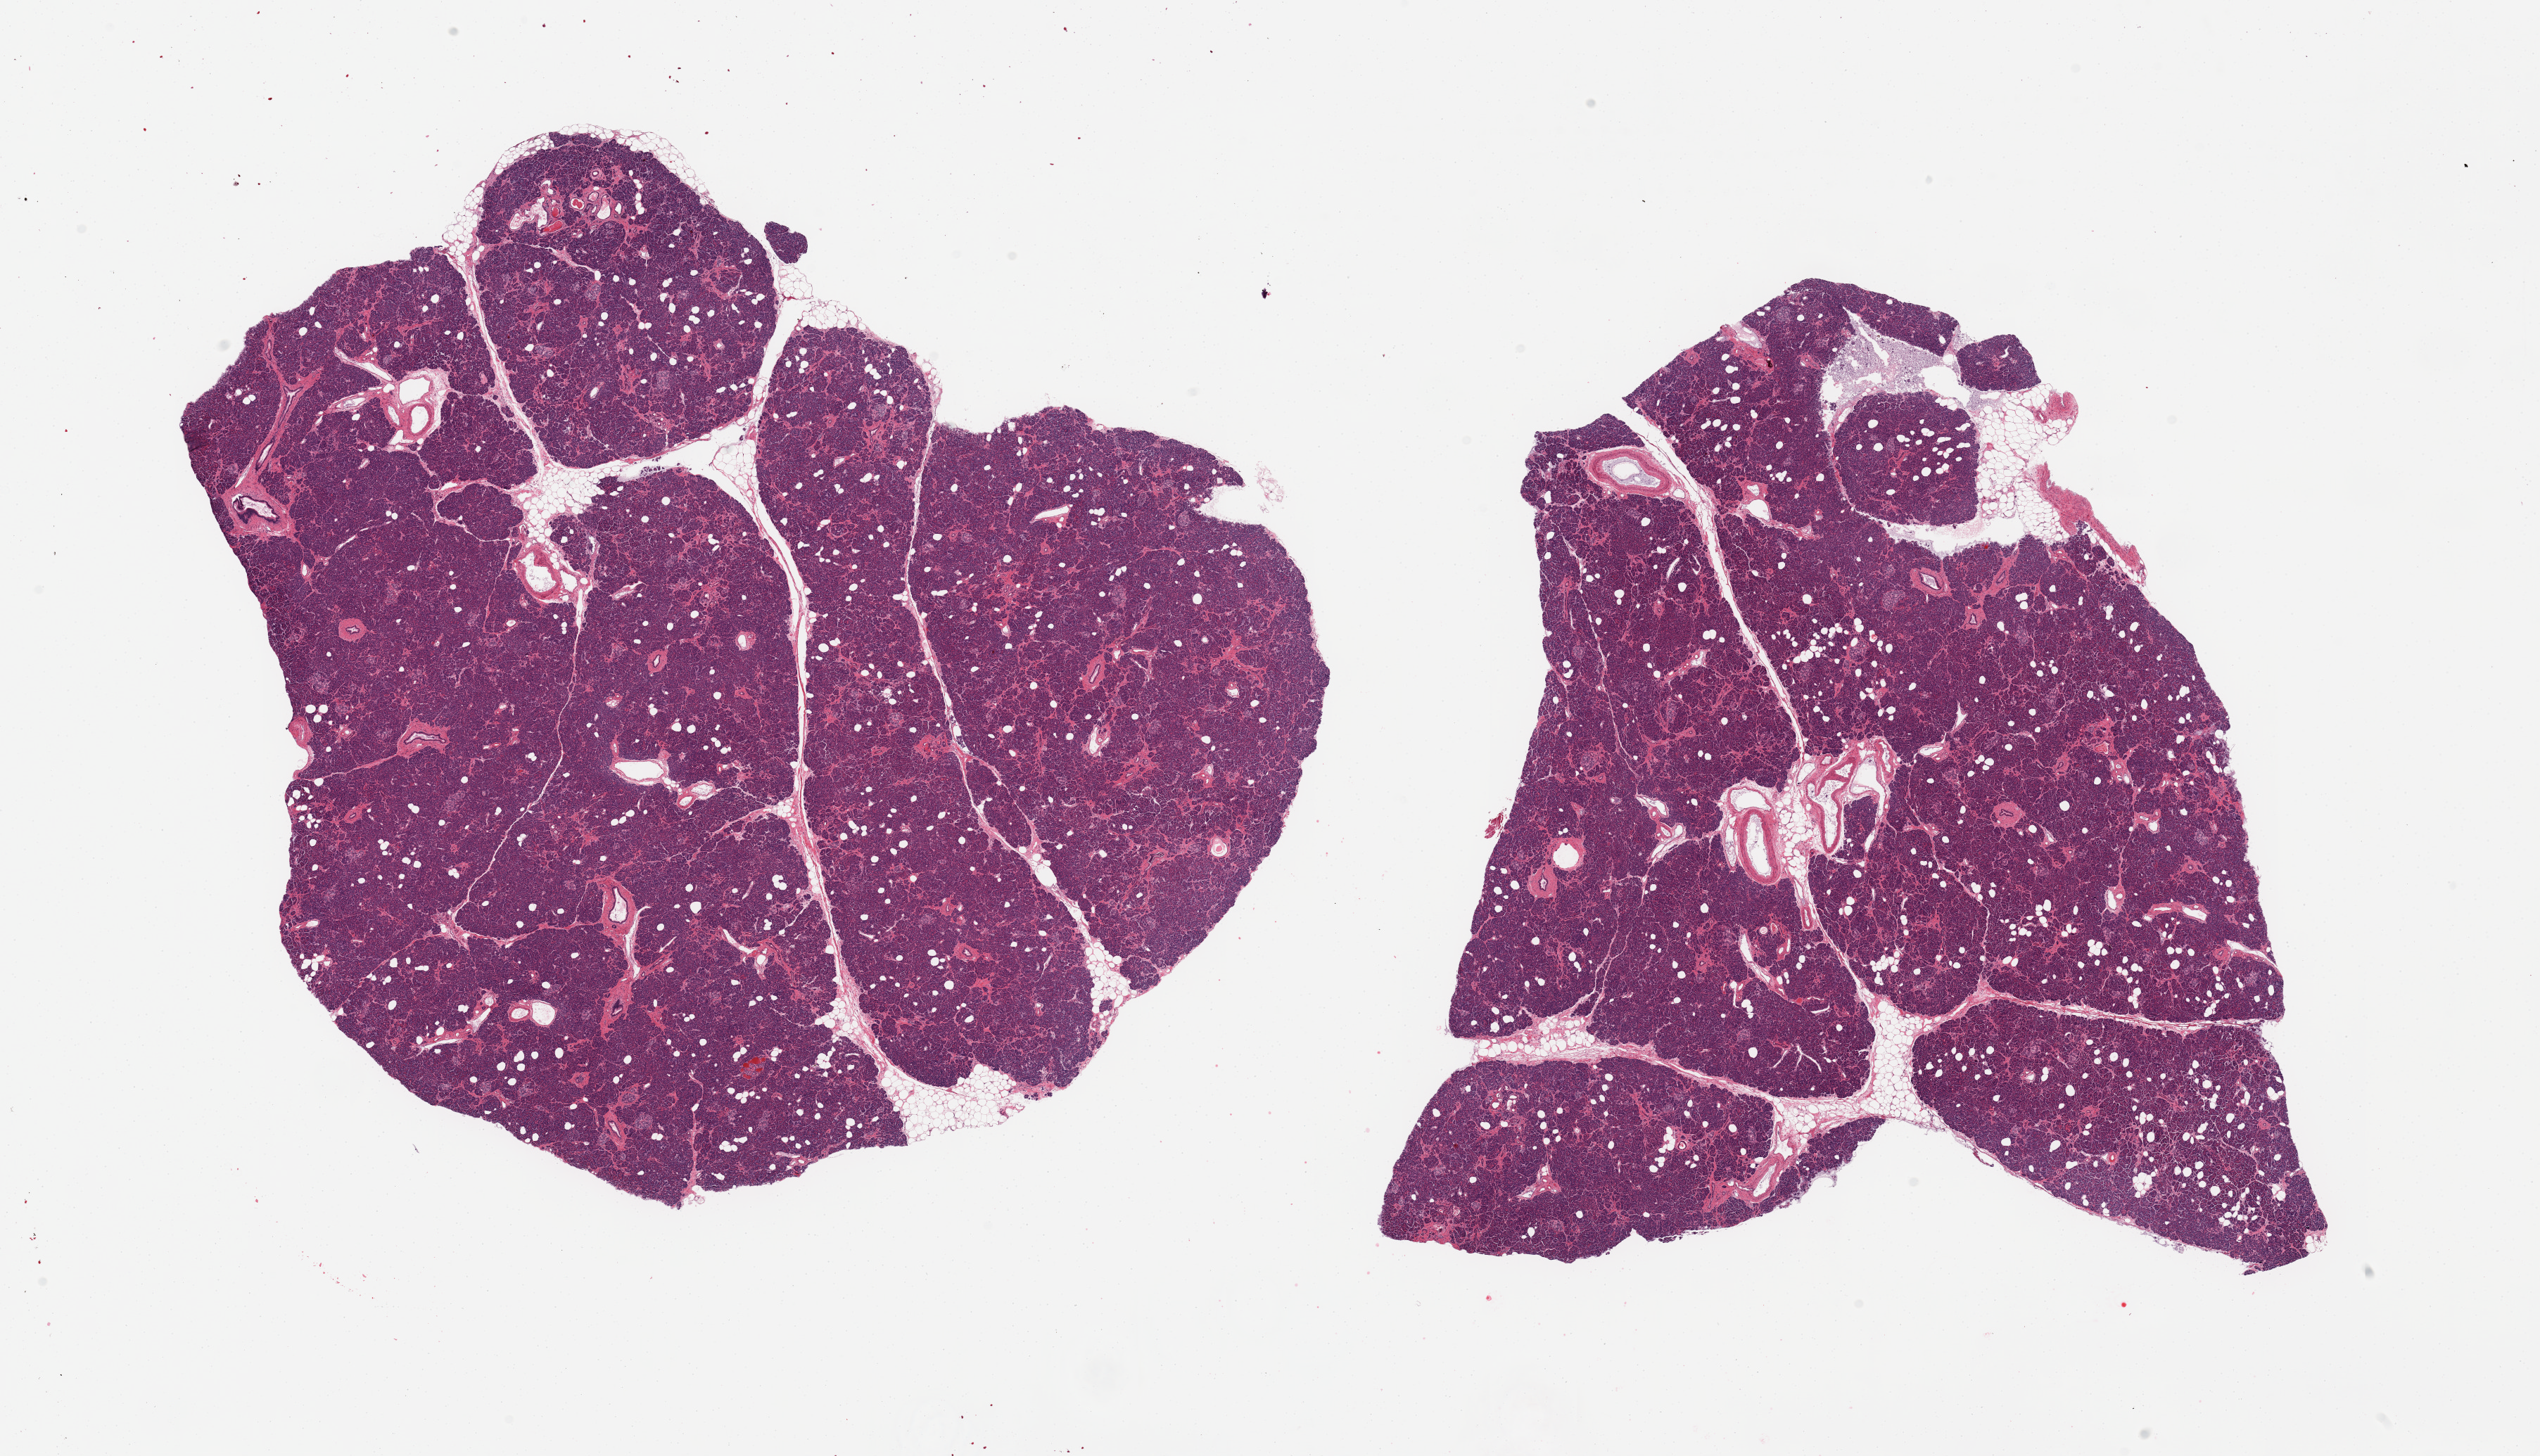
Whole-slide image, hematoxylin and eosin (H&E) stain, a low-resolution overview of the entire scanned area, about 28.5 x 16.4 mm (acquisition: 20x scan). PAXgene-fixed paraffin-embedded (PFPE) section. Sampled site (target tissue): pancreas. Tissue donor sample. Donor: male.
Review note (as recorded): 2 pieces; islets well visualized, some fibrosis.